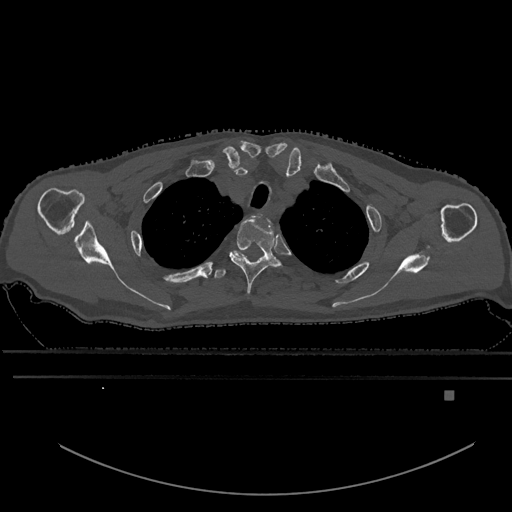
CT including the spine, one axial slice; slice 491 of 969 in the series (ordered by position); bone window (W 1800 / L 400 HU); 0.5 mm slice thickness; 512 × 512 image matrix, field of view 456 × 456 mm. Patient: male, 82 years. From the clinical record (not read from this slice): primary cancer: prostate.
Structures marked on this image (semi-automatic segmentation, software-assisted and operator-edited):
- T1 vertebra: box from (x=260, y=214) to (x=262, y=216) px
- T2 vertebra: (x=229, y=215)–(x=286, y=295)
- T3 vertebra: (x=214, y=253)–(x=244, y=279)